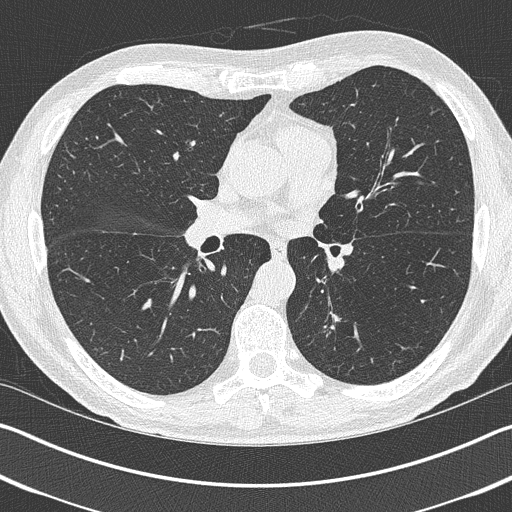
Low-dose screening chest CT, one axial slice; position 224 of 402 along the scan axis; 120 kVp; lung window (W 1500 / L -600 HU); 1 mm slice thickness; 512 × 512 image matrix.
Structures marked on this image (manually delineated by an expert):
- lesion 1 (tumor, lower lobe of left lung): bounding box [x1, y1, x2, y2] px = [324, 312, 340, 330]